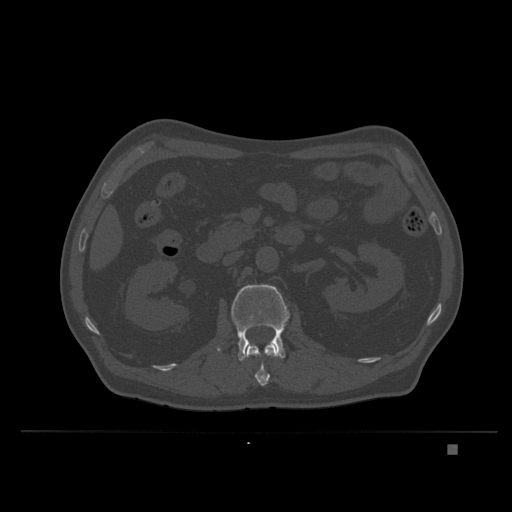
CT including the spine, one axial slice; position 125 of 435 along the scan axis; bone window (W 1800 / L 400 HU); 1.5 mm slice thickness; 512 × 512 image matrix, field of view 434 × 434 mm. Male patient, age 73 years. From the clinical record (not read from this slice): primary cancer: skin.
Outlined on this slice (semi-automatically segmented with operator editing):
- L1 vertebra: box from (x=243, y=341) to (x=278, y=386) px
- L2 vertebra: (x=216, y=284)–(x=290, y=361)